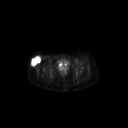
FDG PET of an extremity soft-tissue mass (from a PET/CT study), one axial slice; position 61 of 267 along the scan axis; 3.27 mm slice thickness; 128 × 128 image matrix, field of view 700 × 700 mm. Patient: female, 34 years. From the clinical record (not read from this slice): histological type: synovial sarcoma; grade: intermediate; site of the primary tumour: right thigh.
Outlined on this slice (expert contour drawn on MRI and transferred to this co-registered scan by the dataset authors):
- gross tumour volume including surrounding oedema: bounding box (x1, y1, x2, y2) in pixels: (30, 56, 41, 67)
- gross tumour volume (mass): (30, 56, 41, 67)